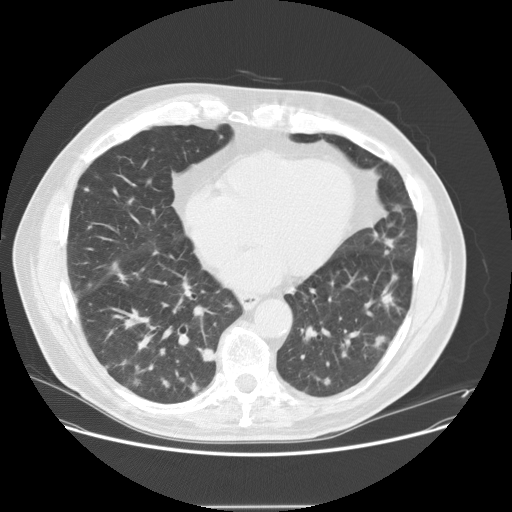
Low-dose screening chest CT, one axial slice; reconstruction kernel STANDARD; 120 kVp; lung window (W 1500 / L -600 HU); 512 × 512 image matrix.
Annotated regions visible in this slice (manually delineated by an expert):
- lesion 1 (tumor, lower lobe of right lung): box from (x=203, y=348) to (x=214, y=362) px